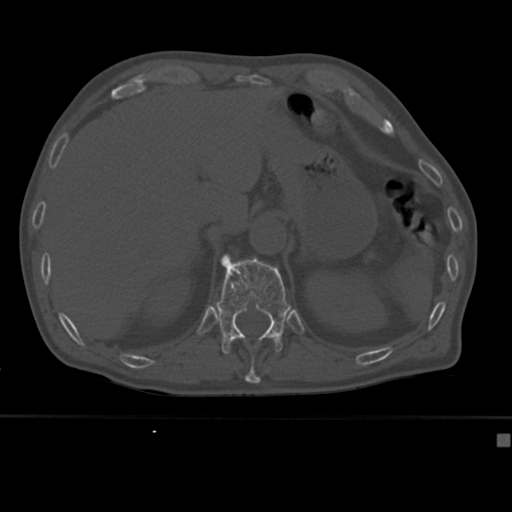
CT including the spine, one axial slice; position 195 of 430 along the scan axis; bone window (W 1800 / L 400 HU); 512 × 512 image matrix, field of view 337 × 337 mm. Male patient, age 64 years. Case-level facts recorded for this patient, not image findings: primary cancer: uterus; vertebrae with lytic lesions (as recorded): T1, T4, T5, T7, L5.
Outlined on this slice (semi-automatically segmented with operator editing):
- T11 vertebra: bounding box <245,356,261,382> (left, top, right, bottom; pixels)
- T12 vertebra: <215,254,291,354>